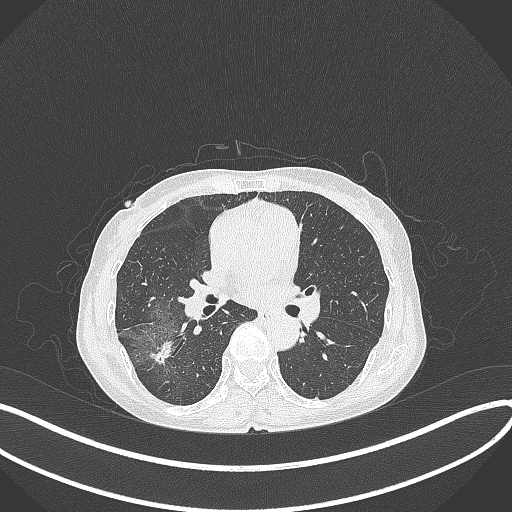
Chest CT, one axial slice; position 211 of 371 along the scan axis; reconstruction kernel B70f; 120 kVp; lung window (W 1500 / L -600 HU); 1 mm slice thickness; 512 × 512 image matrix, field of view 400 × 400 mm. Patient: female, 69 years. Case-level facts recorded for this patient, not image findings: clinical TNM (as recorded): T1b N0 M0; histopathological grade: G2-3.
Annotated regions visible in this slice (rectangle marked by the reading radiologist):
- lung tumour (recorded histology: adenocarcinoma): box from (x=148, y=336) to (x=176, y=366) px